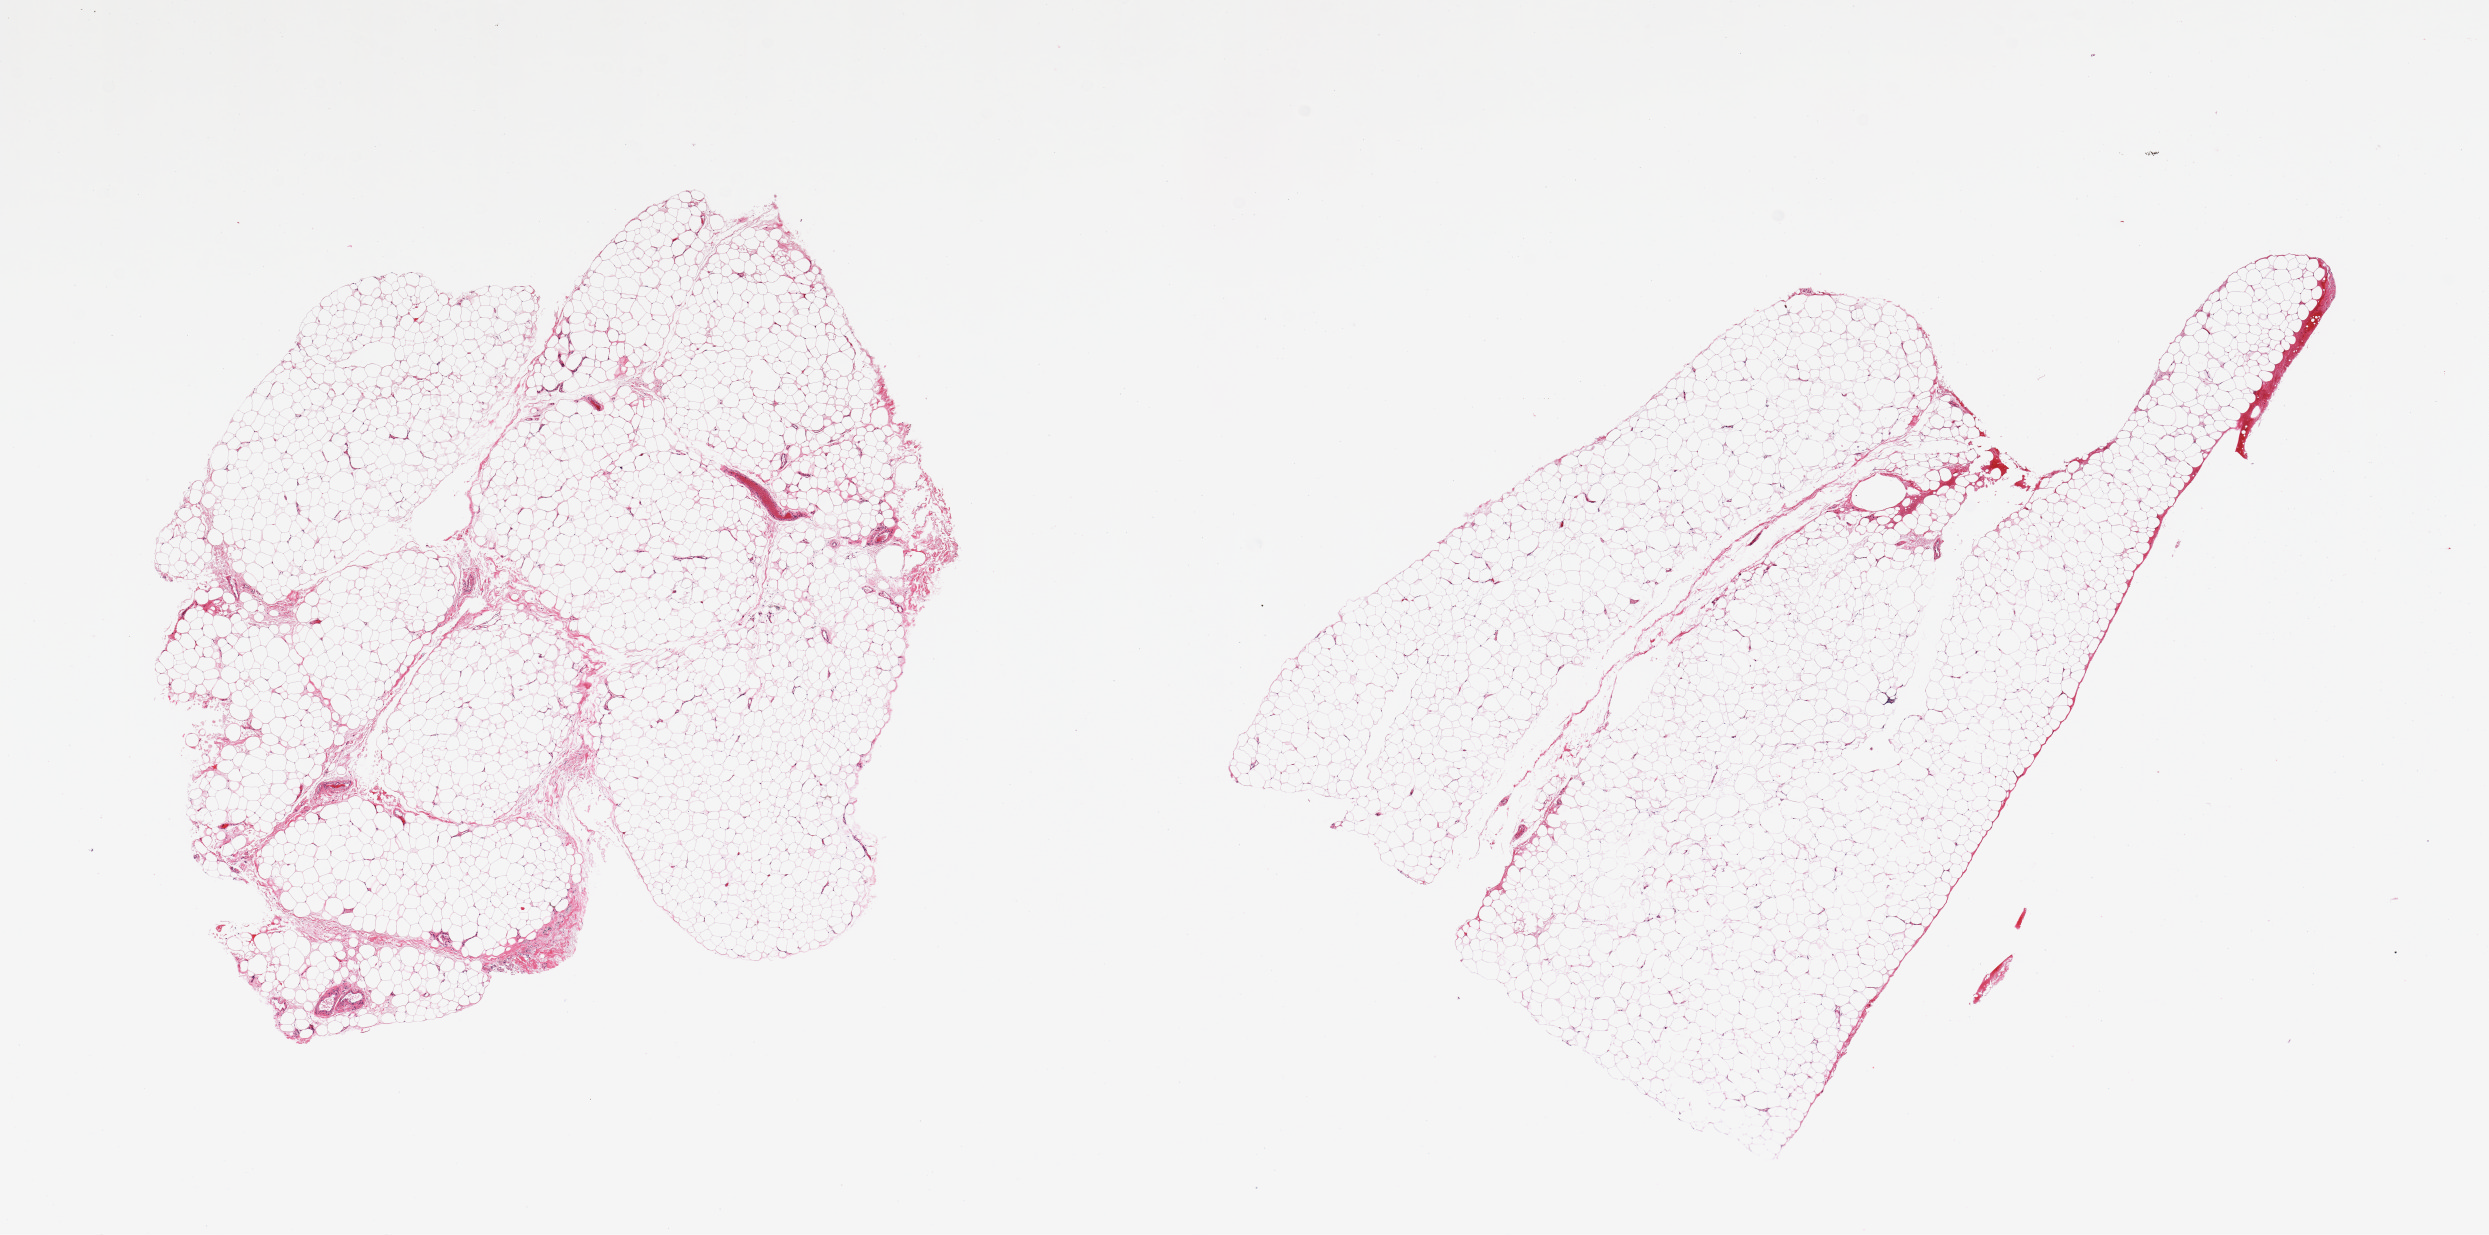
H&E whole-slide image, a low-resolution overview of the entire scanned area, about 19.7 x 9.8 mm, PAXgene-fixed, paraffin-embedded tissue, sampled site (target tissue): adipose tissue, tissue donor sample. Donor sex: male.
- review note (as recorded): 2 pieces, trace fascia/vascular elements